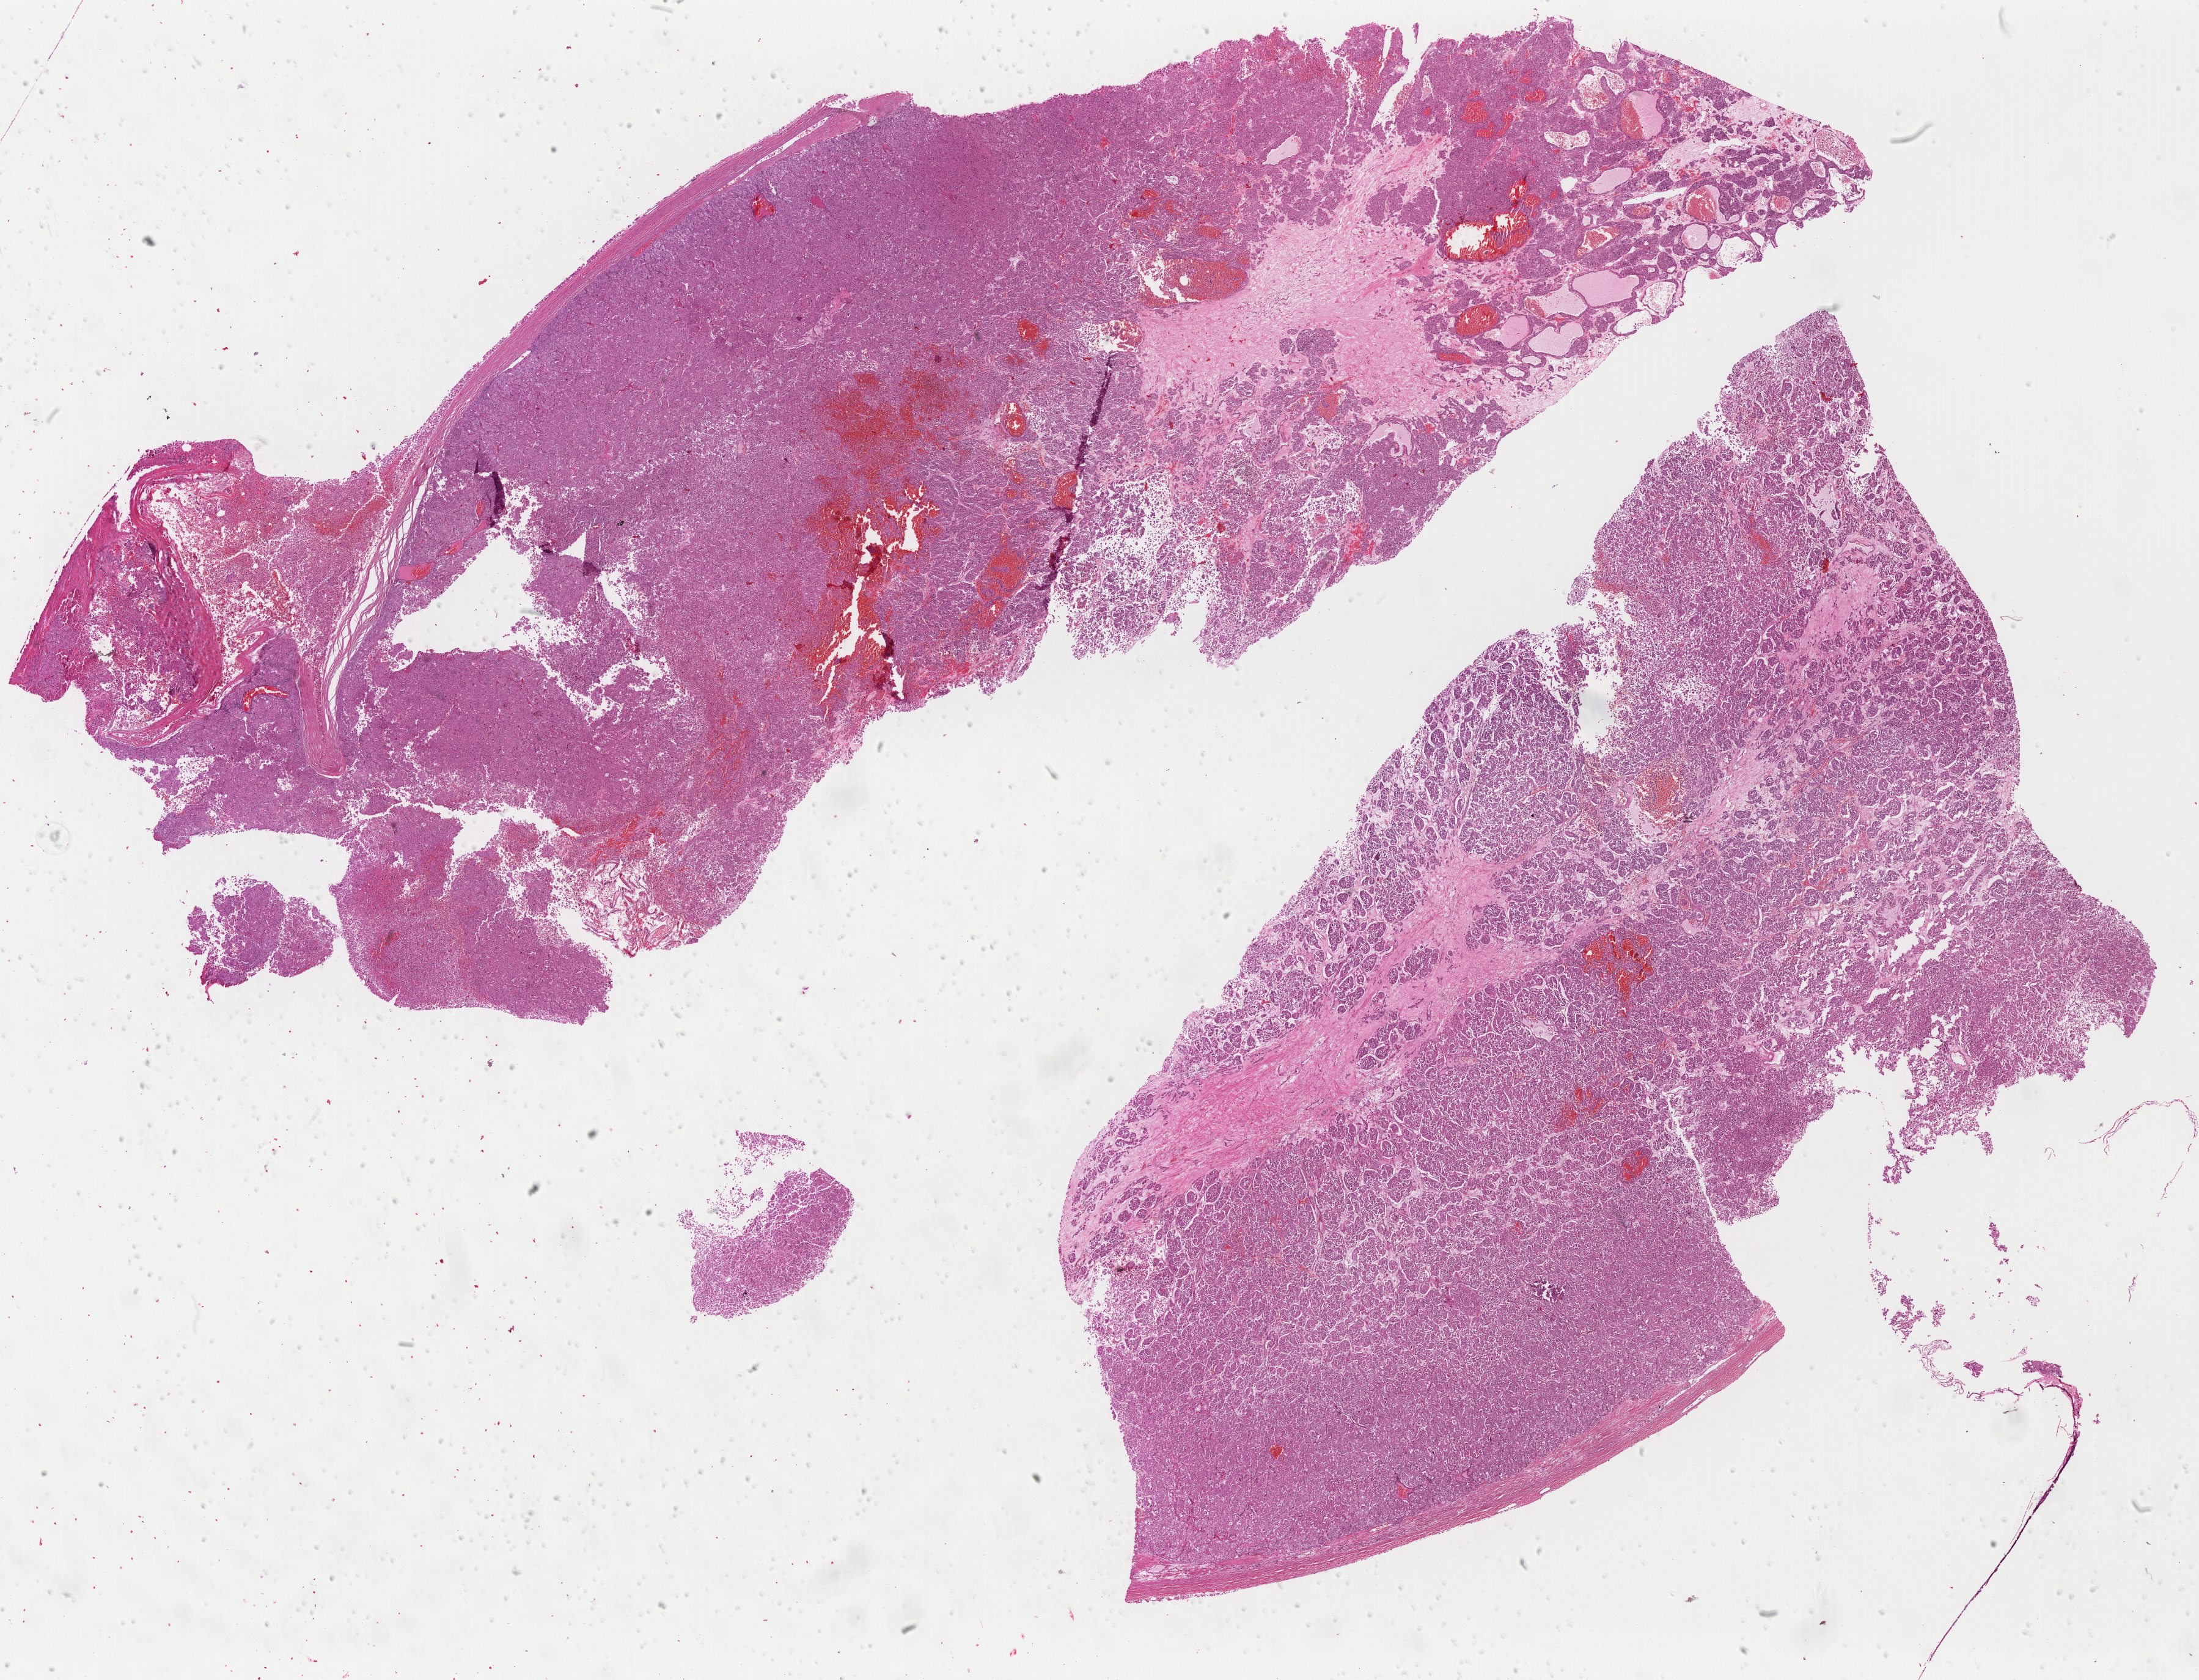
Digitized Hematoxylin and eosin (H&E) stained tissue section (whole slide), a low-resolution overview of the entire scanned area, about 29.0 x 22.2 mm. Formalin-fixed paraffin-embedded (FFPE) diagnostic section. Kidney, primary tumour sample. Patient: male, age at initial diagnosis 62 years.
AJCC pathologic stage: II. Diagnosis: Renal cell carcinoma, chromophobe type. TNM: T2 NX.